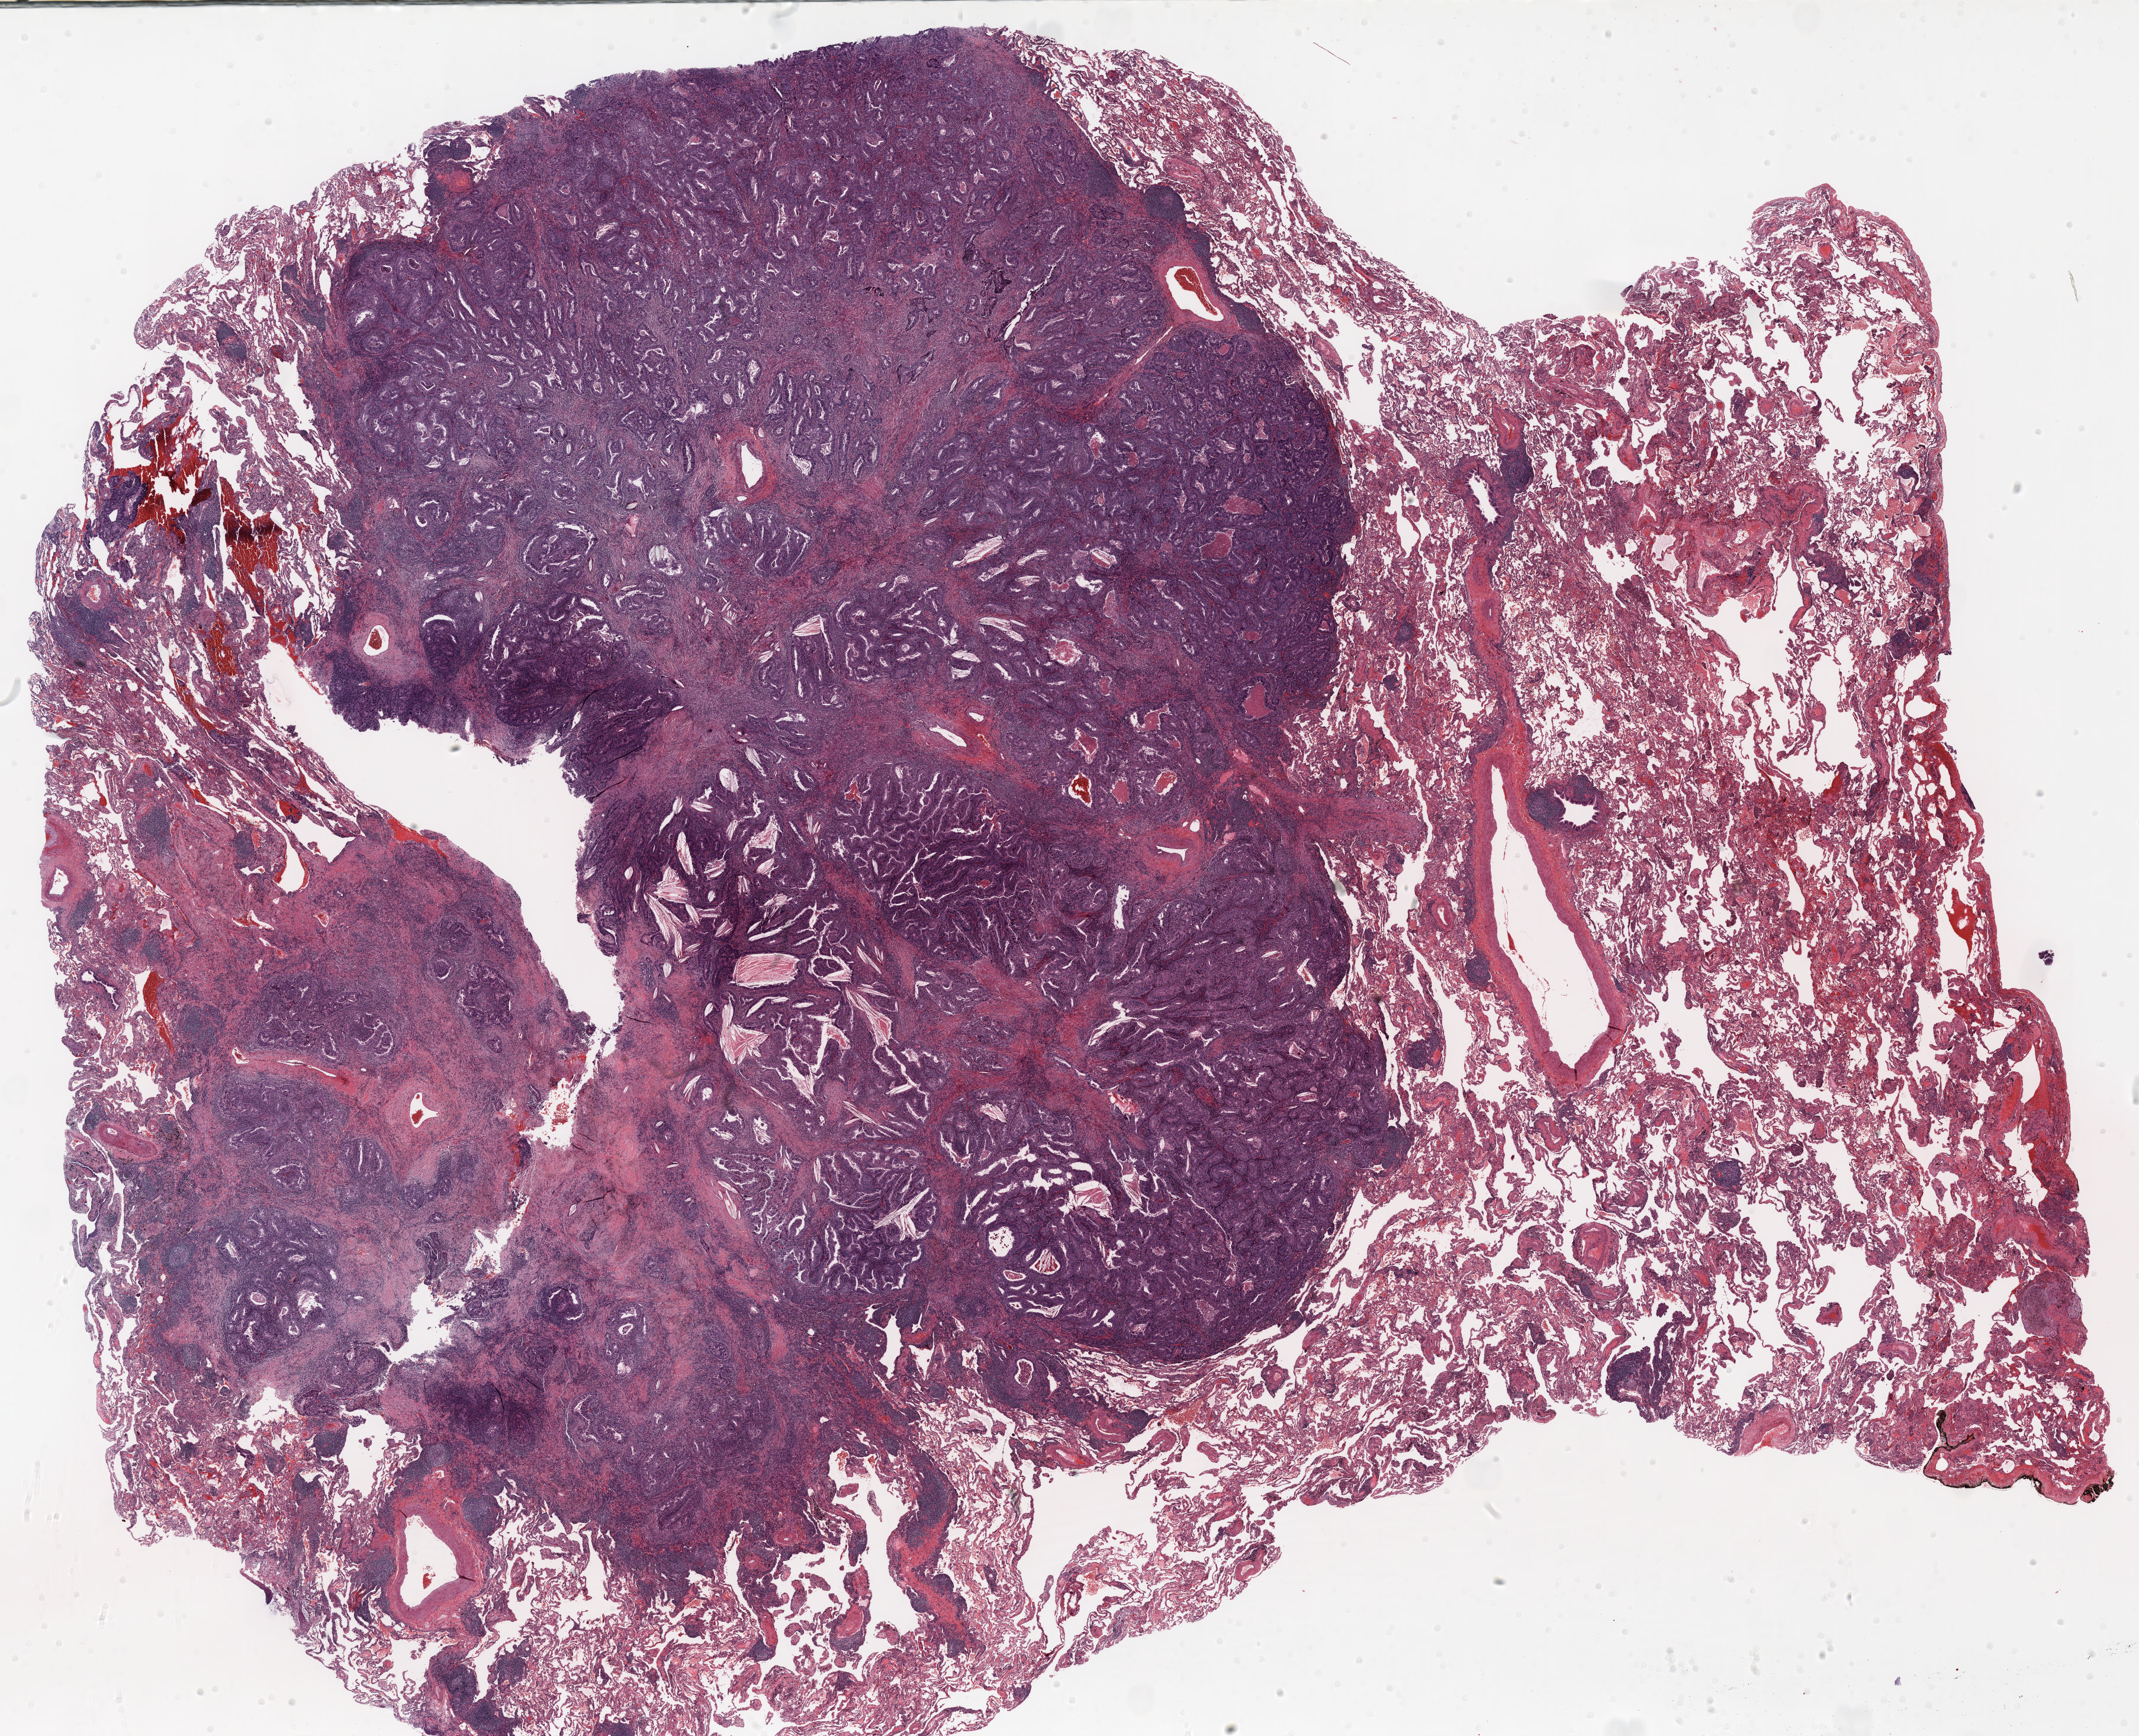
Whole-slide histology image, H&E-stained, whole scanned area (about 29.0 x 23.6 mm) shown as a low-resolution overview, formalin-fixed paraffin-embedded (FFPE) section, lung. Female, age 72 at enrolment. Former smoker at enrolment. Grade: moderately differentiated (G2).
- stage (AJCC 6th edition): IA
- primary tumour location (clinical record): left upper lobe
- participant's lung-cancer diagnosis: Adenocarcinoma, NOS
- tumour size (pathology): 25 mm
- note: participant had 2 primary lung cancers recorded; fields above describe the first